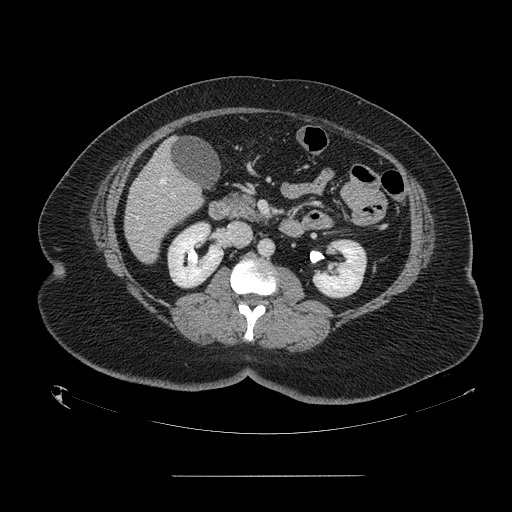
Contrast-enhanced abdominal CT, one axial slice. Position 58 of 164 along the scan axis. 120 kVp. Intravenous contrast given. Soft-tissue window (W 400 / L 40 HU). 2.5 mm slice thickness. 512 × 512 image matrix. Female patient, age 52 years. From the clinical record (not read from this slice): diagnosis: colorectal cancer liver metastases, imaged before liver resection.
Annotated regions visible in this slice (outlined manually by an expert reader):
- hepatic veins: bounding box (x1, y1, x2, y2) in pixels: (136, 178, 166, 229)
- liver: (125, 143, 204, 263)
- portal vein (with intrahepatic branches): (171, 193, 174, 197)